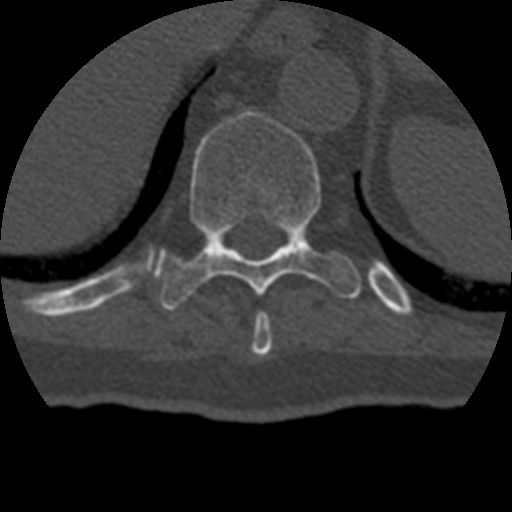
CT including the spine, one axial slice. Position 219 of 399 along the scan axis. 120 kVp. Bone window (W 1800 / L 400 HU). 1.25 mm slice thickness. 512 × 512 image matrix, field of view 160 × 160 mm. Patient age 69 years. Case-level facts recorded for this patient, not image findings: primary cancer: prostate.
Structures marked on this image (semi-automatic segmentation, software-assisted and operator-edited):
- T10 vertebra: box from (x=158, y=112) to (x=361, y=311) px
- T9 vertebra: (x=252, y=312)–(x=273, y=357)